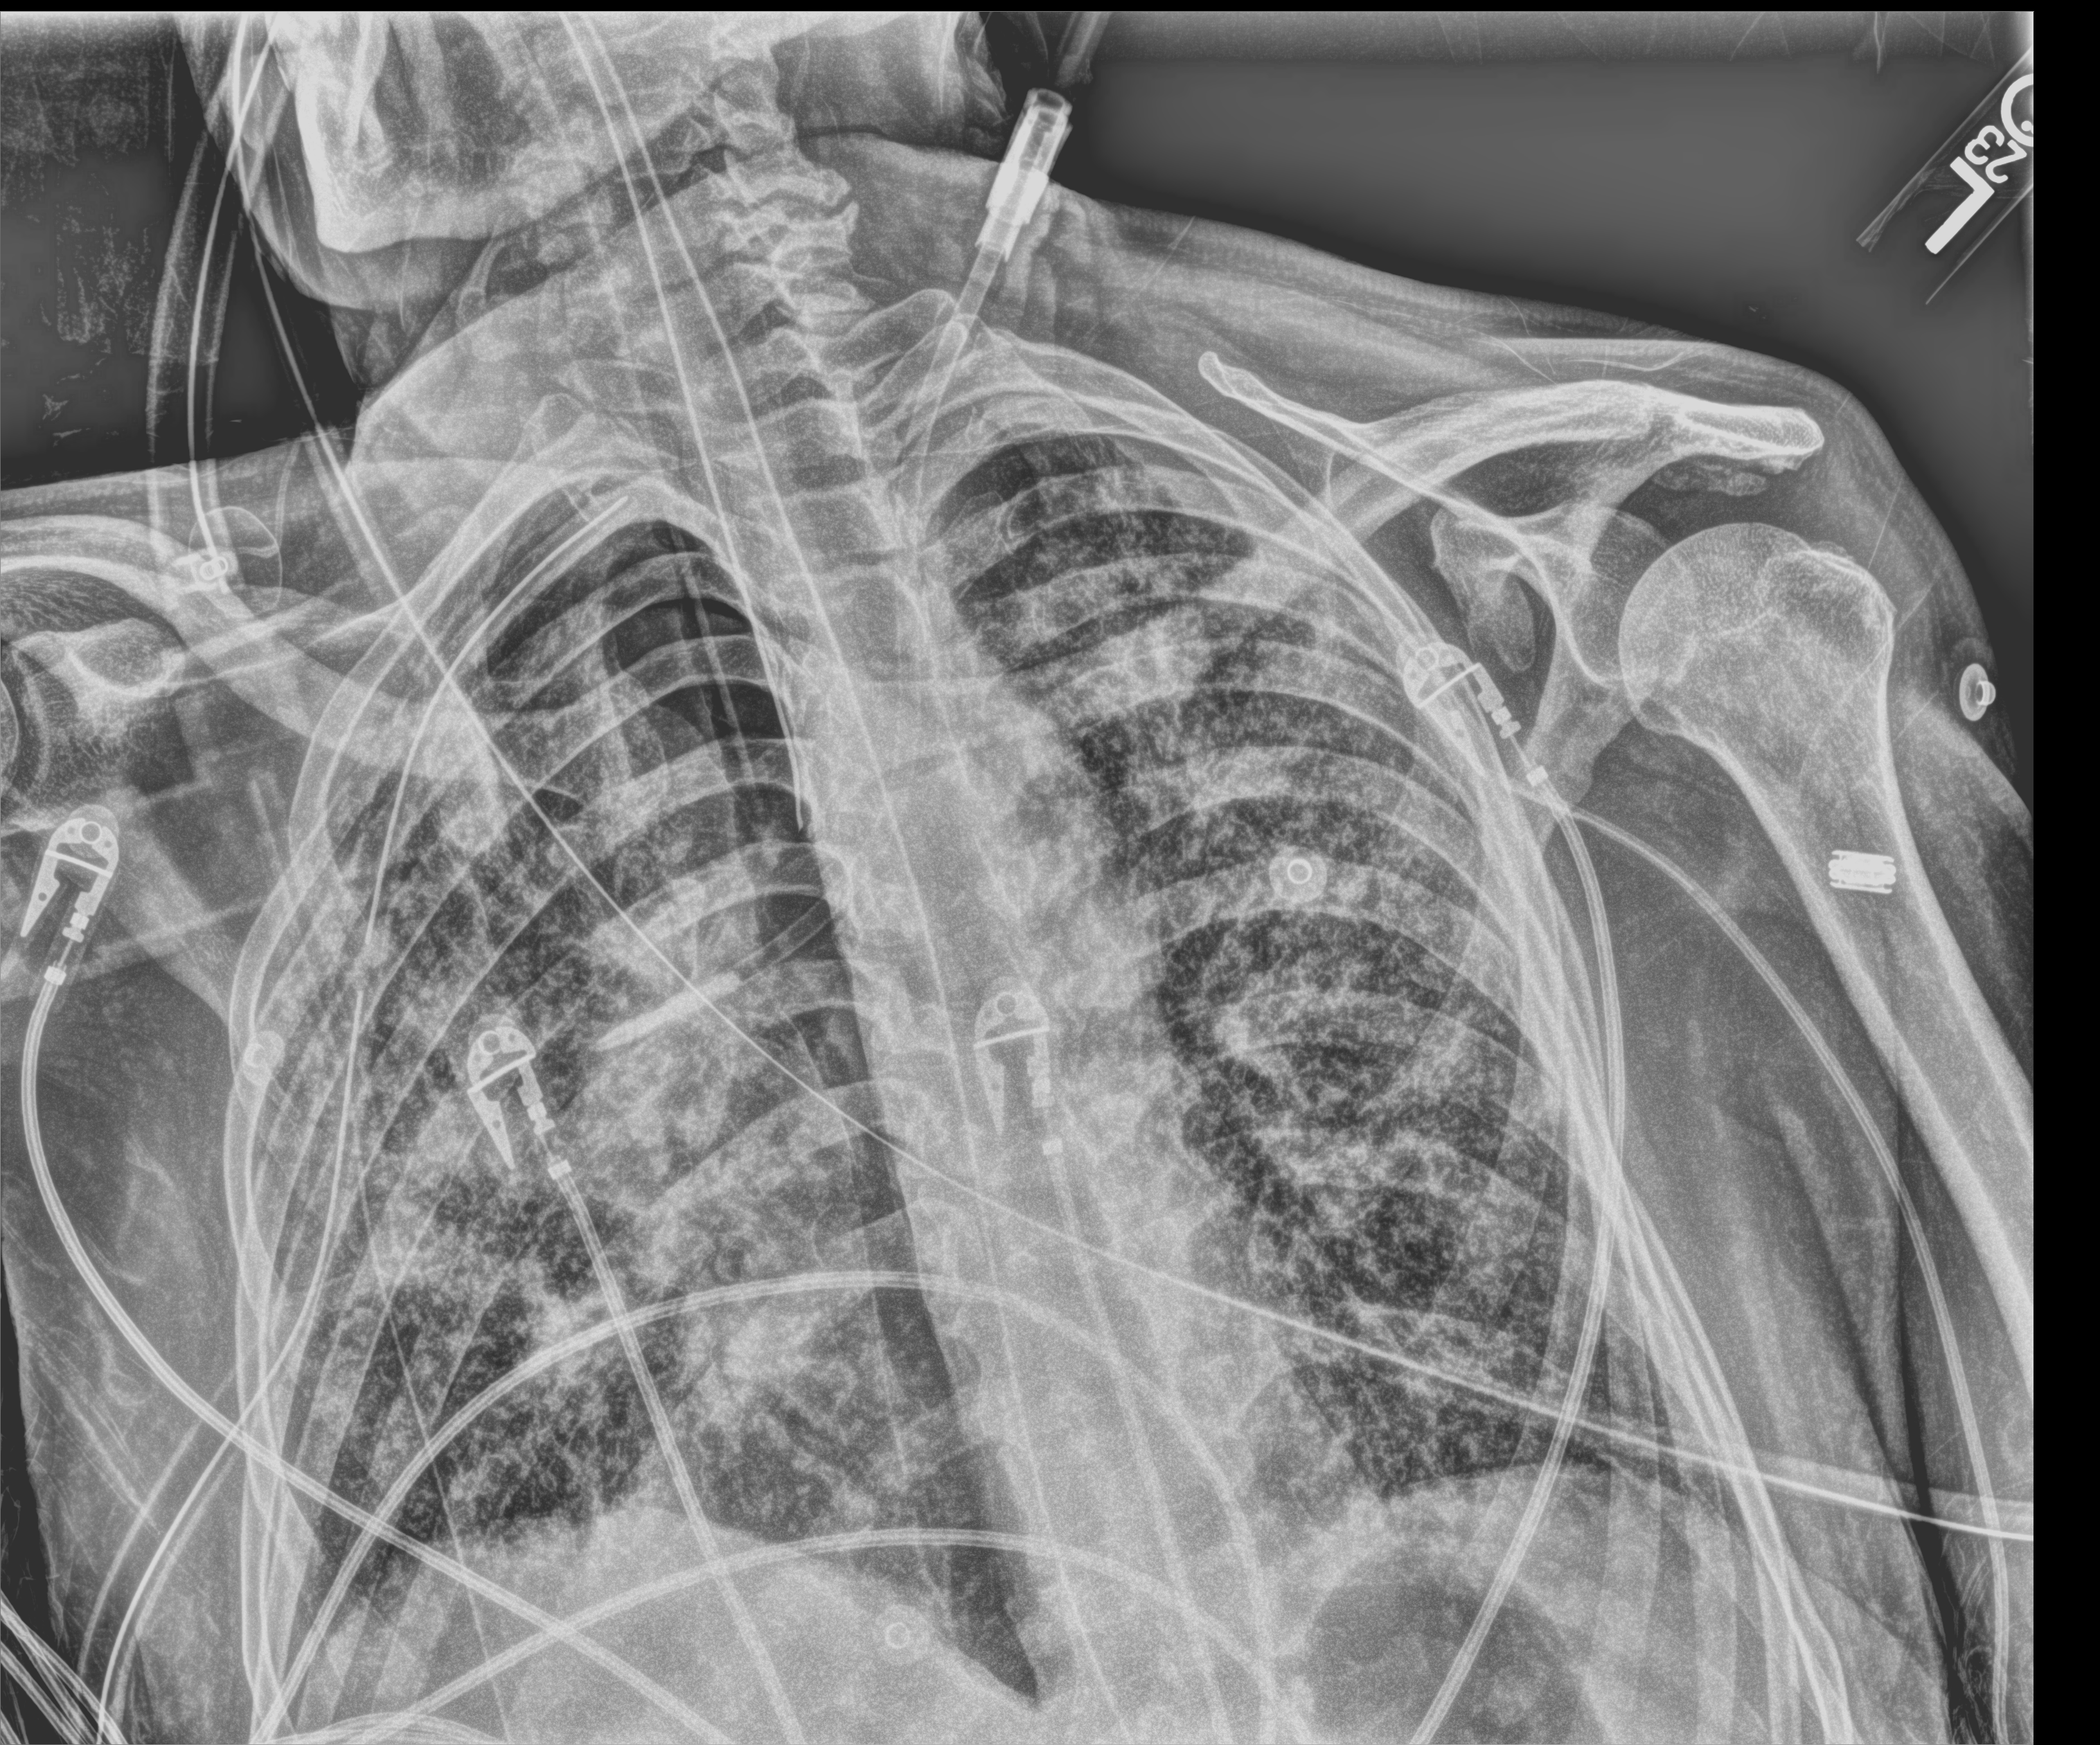
Chest X-ray (portable); anteroposterior (AP) projection. Patient hospitalised with COVID-19; male, aged 60–74 years.
Admission-level facts for this patient (not findings on this image; timing relative to this image not recorded):
- chronic kidney disease (admission record): no
- length of hospital stay: 65 days